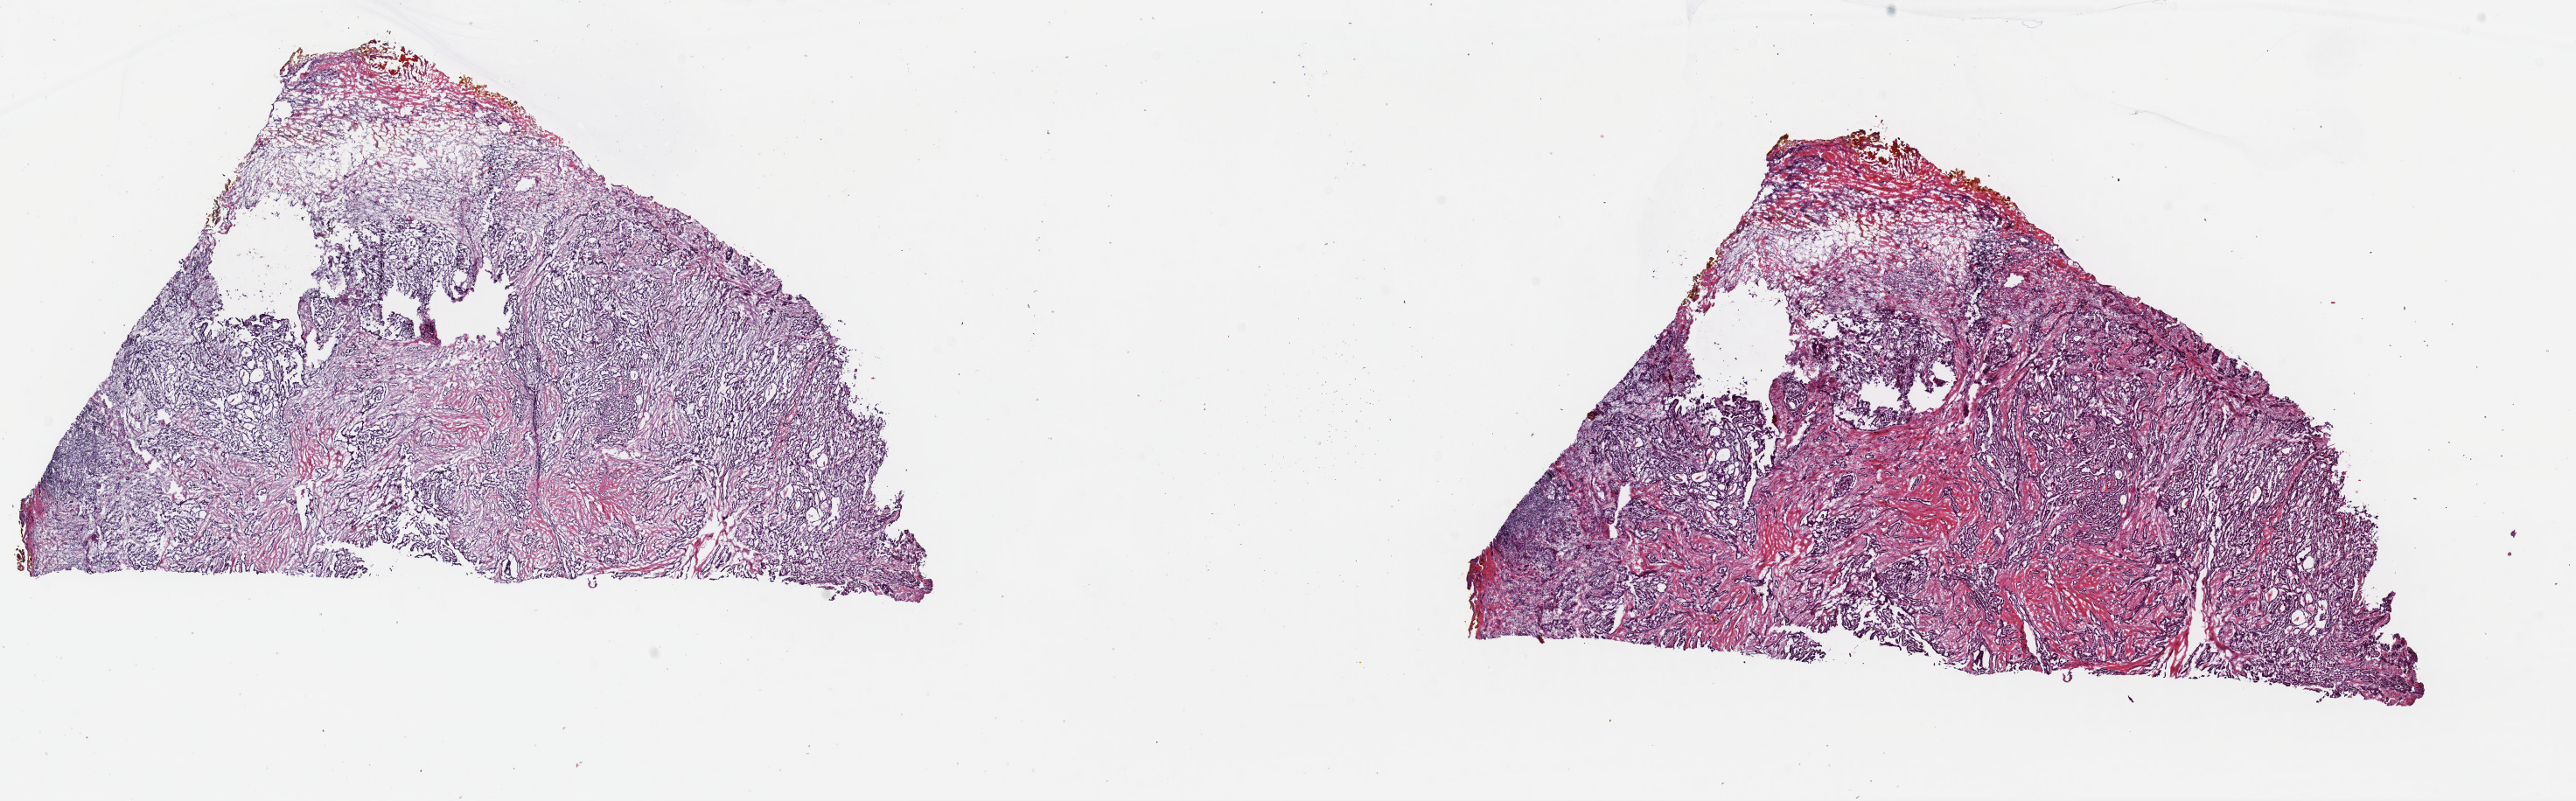
Hematoxylin and eosin (H&E) stained whole-slide image, a low-resolution overview of the entire scanned area, about 23.3 x 7.2 mm, frozen section from the top of the tissue portion, primary tumour sample from the thyroid. Patient: female, age at initial diagnosis 33 years. Composition of this section per pathologist review: tumour cells 50%, tumour nuclei 100%, normal cells 0%, stromal cells 50%, necrosis 0%. Inflammatory infiltration, as recorded: lymphocyte infiltration 8%, monocyte infiltration 1%, neutrophil infiltration 0%.
Laterality: right. TNM: T3 N1a MX. Diagnosis: Papillary adenocarcinoma, NOS. AJCC pathologic stage: I (6th edition). Lymph nodes positive (case pathology): 5 of 5 examined.